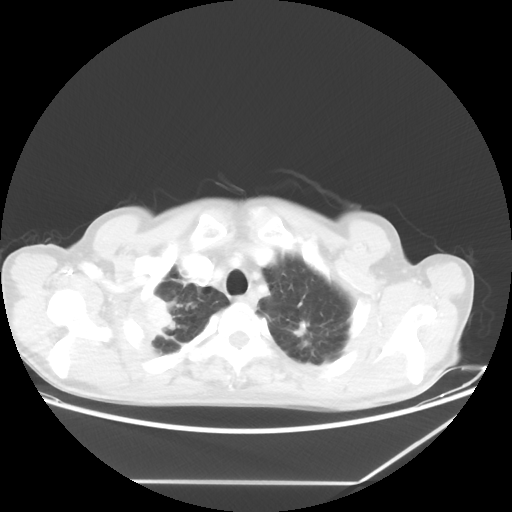
Chest CT, one axial slice; slice 57 of 65 in the series (ordered by position); lung window (W 1500 / L -600 HU); 5 mm slice thickness; 512 × 512 image matrix. Male patient, age 68 years. From the clinical record (not read from this slice): clinical TNM (as recorded): T3 N3 M0.
Annotated regions visible in this slice (bounding box drawn by a radiologist):
- lung tumour (recorded histology: adenocarcinoma): bounding box <132,287,178,345> (left, top, right, bottom; pixels)